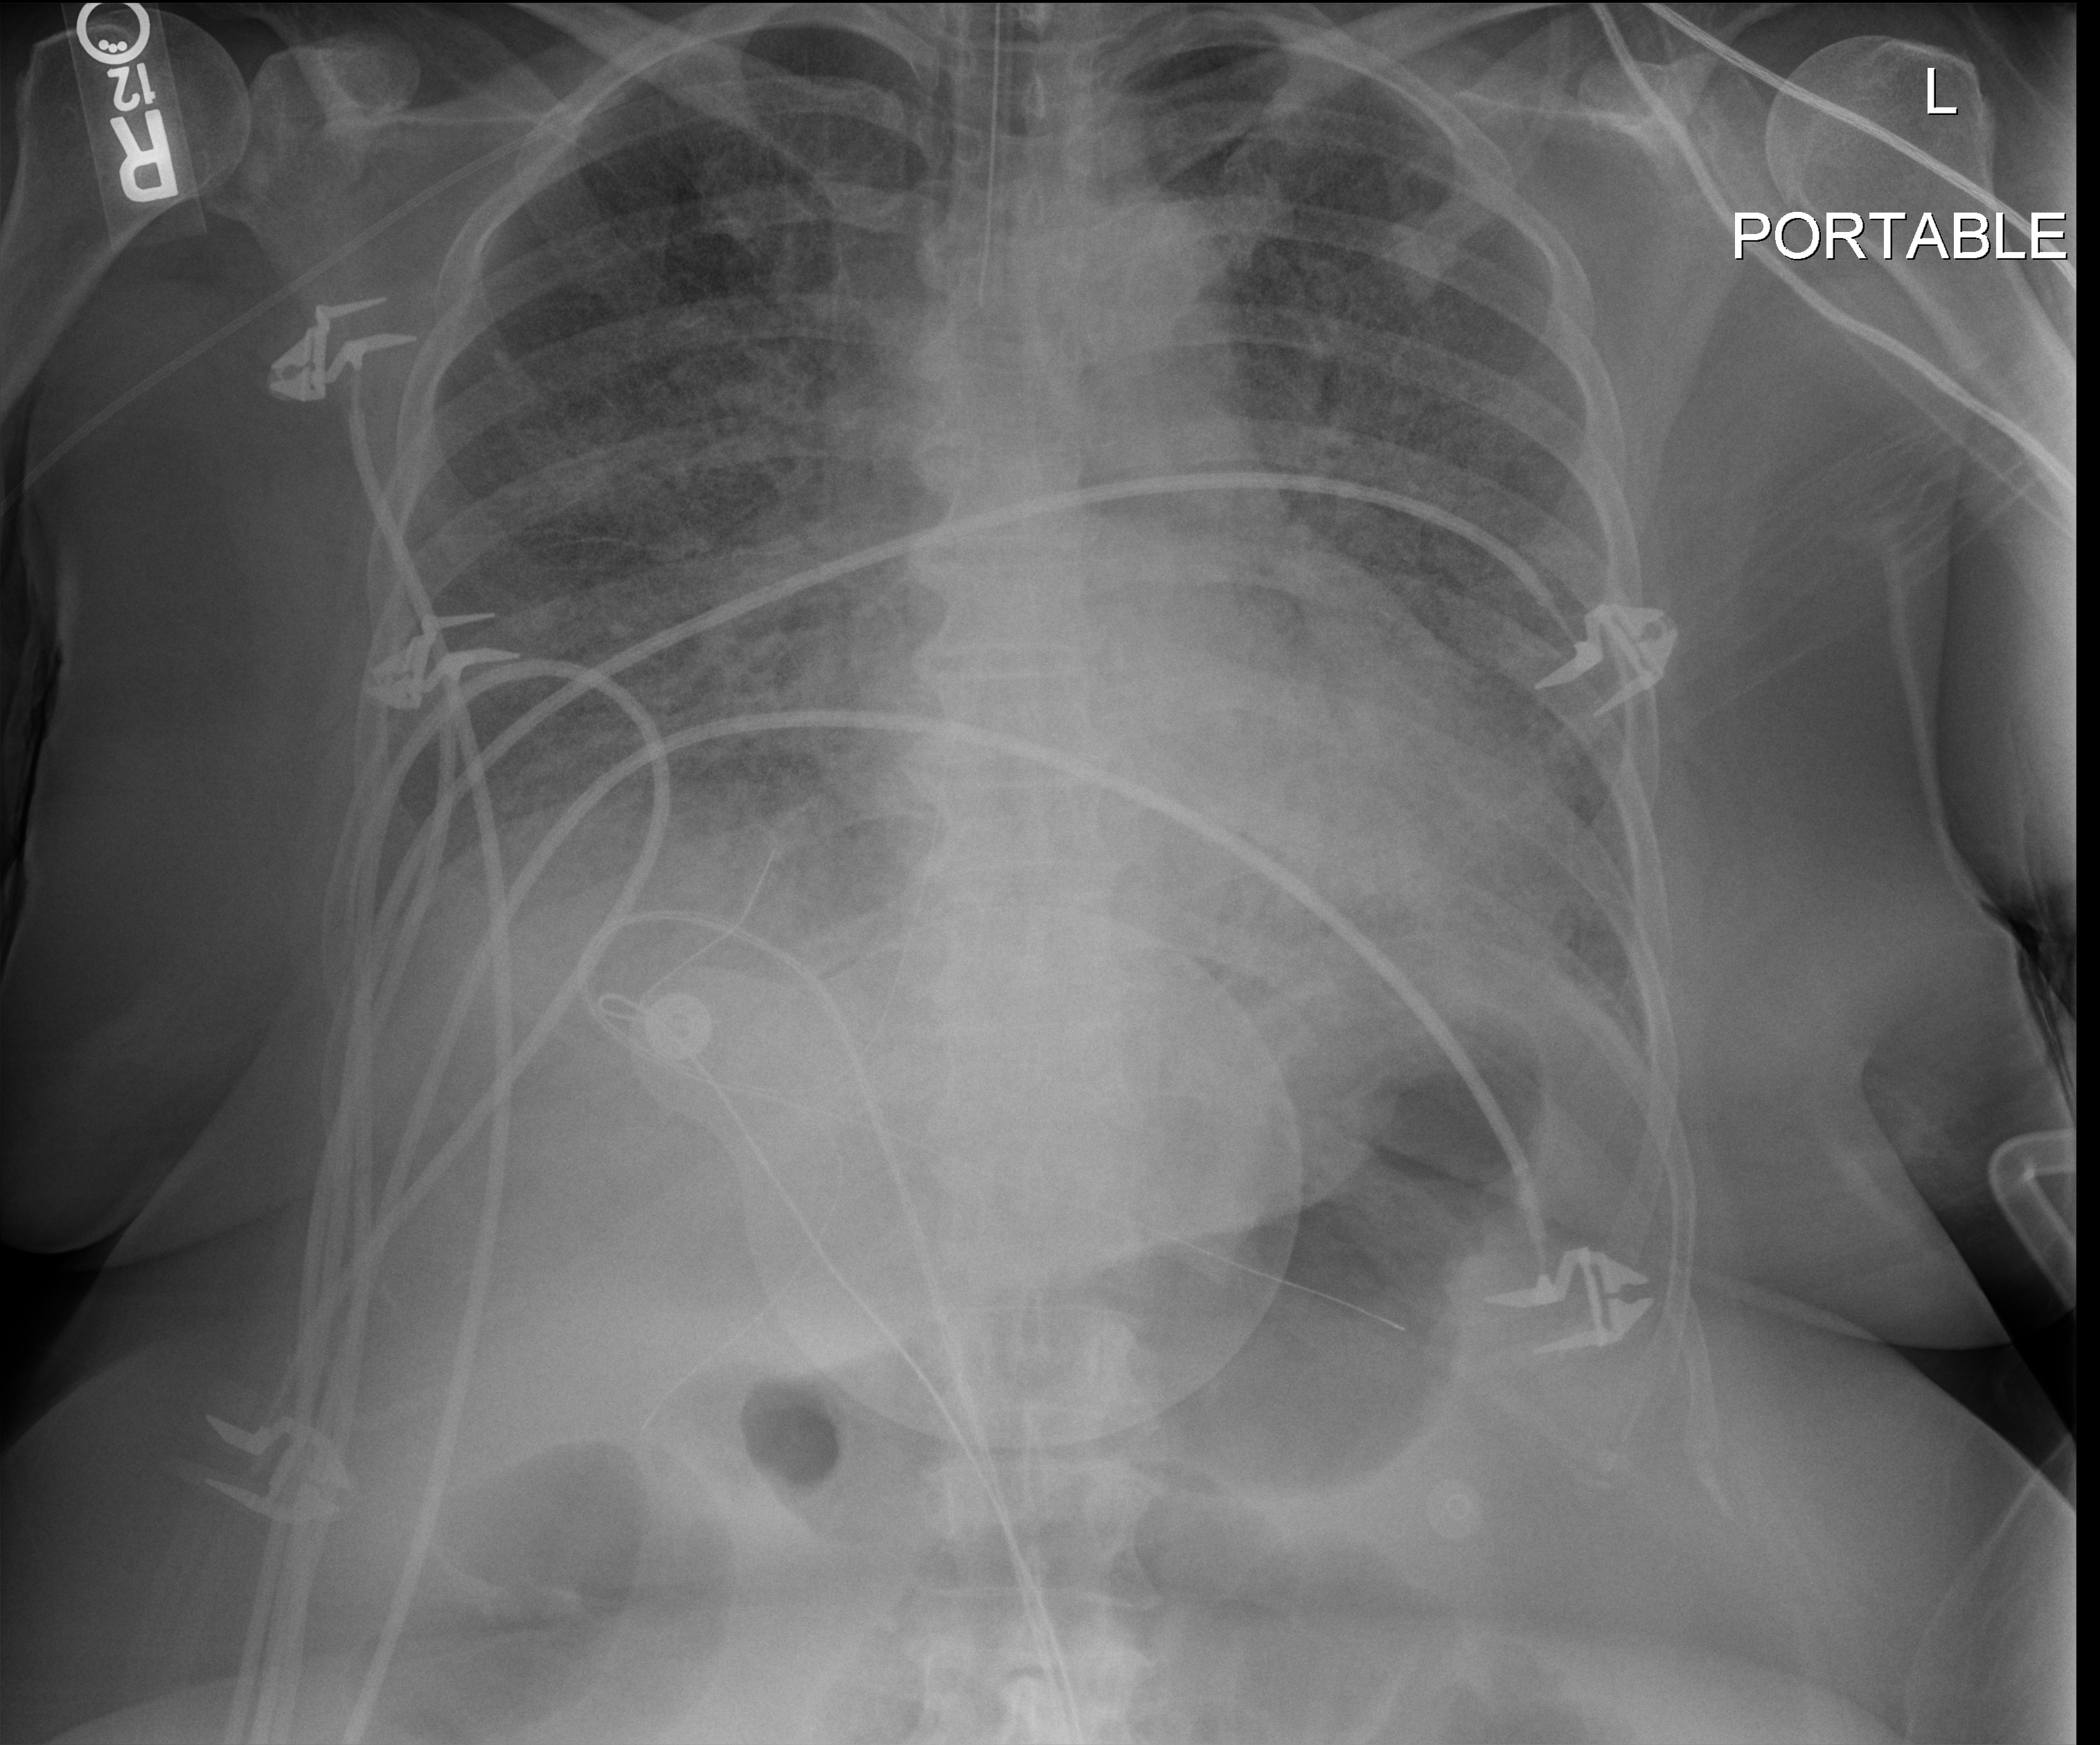
Bedside chest radiograph (digital radiography); anteroposterior (AP) projection. Patient hospitalised with COVID-19; female, aged 60–74 years.
Hospital-stay facts (about this admission, not read from this image; timing relative to this image not recorded):
- length of hospital stay: 38 days
- admitted to intensive care during this hospital stay: yes
- mechanically ventilated during this hospital stay: yes